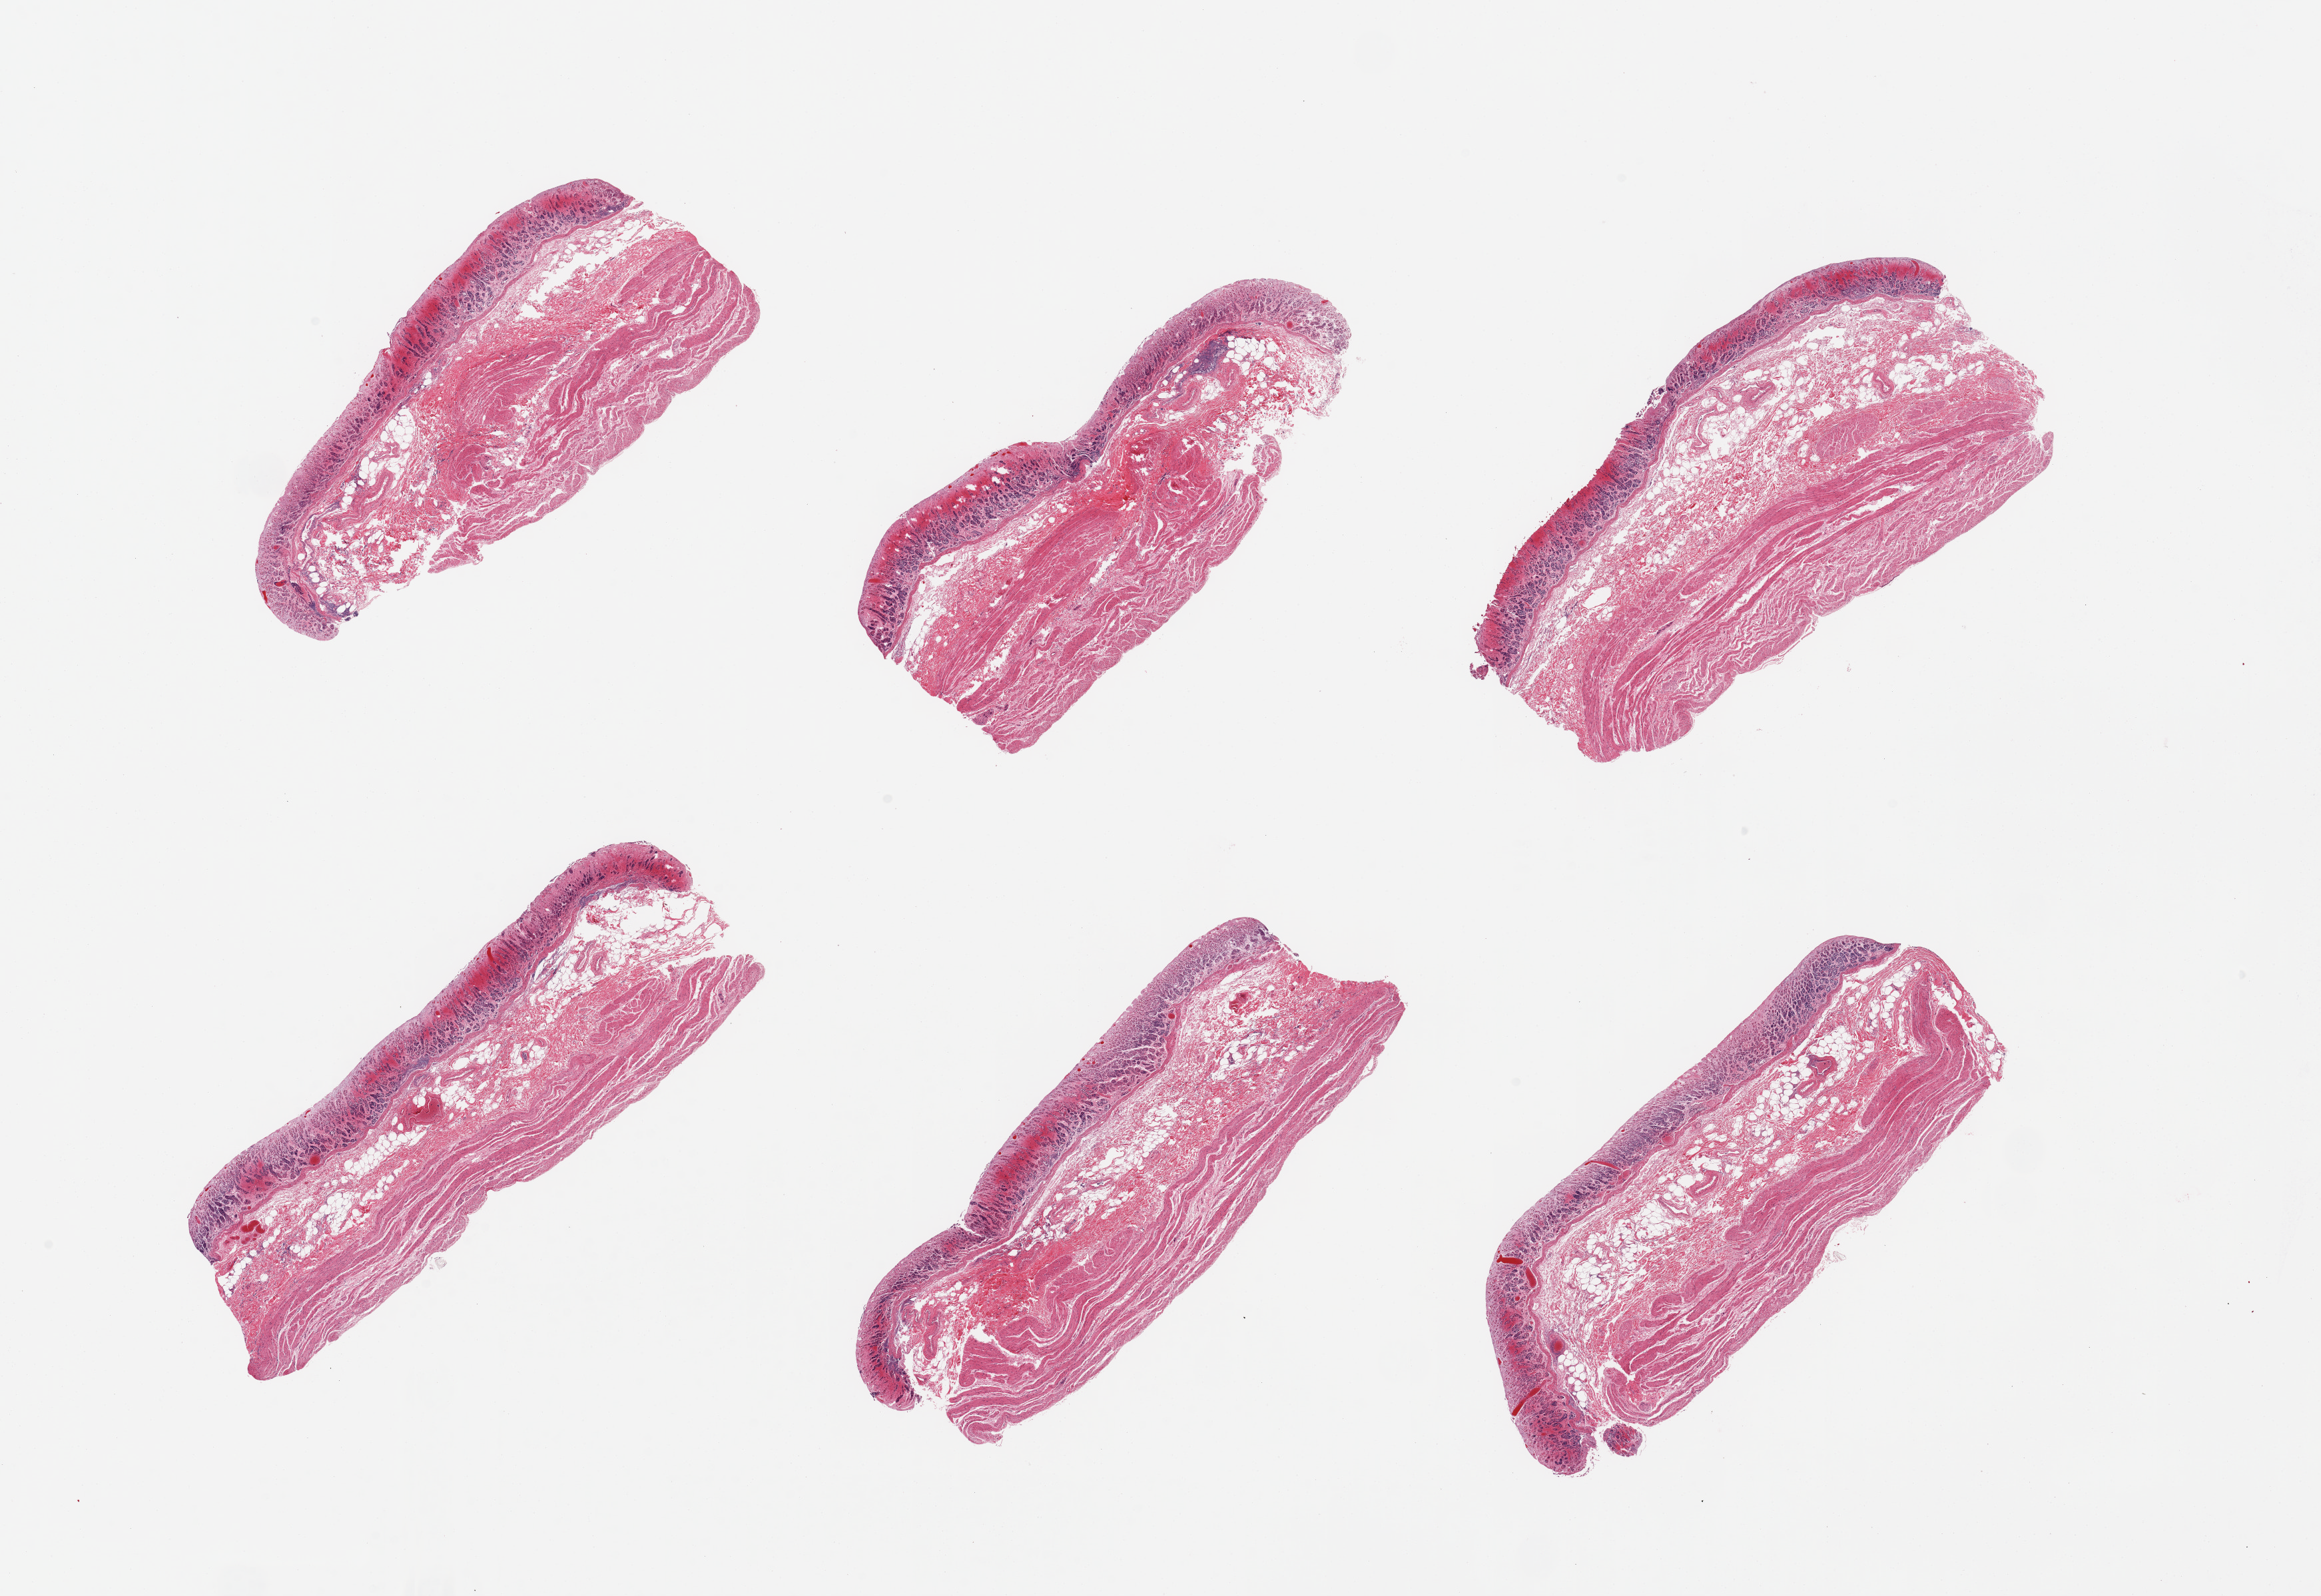
Digitized hematoxylin and eosin (H&E)-stained section, low-resolution overview of the scanned area, about 27.6 x 19.0 mm (slide scanned at 20x), PAXgene-fixed, paraffin-embedded tissue, target tissue: stomach, tissue donor sample. Donor sex: female.
Review note (as recorded): 6 pieces; autolyzed and hemorrhagic mucosa; muscularis intact.